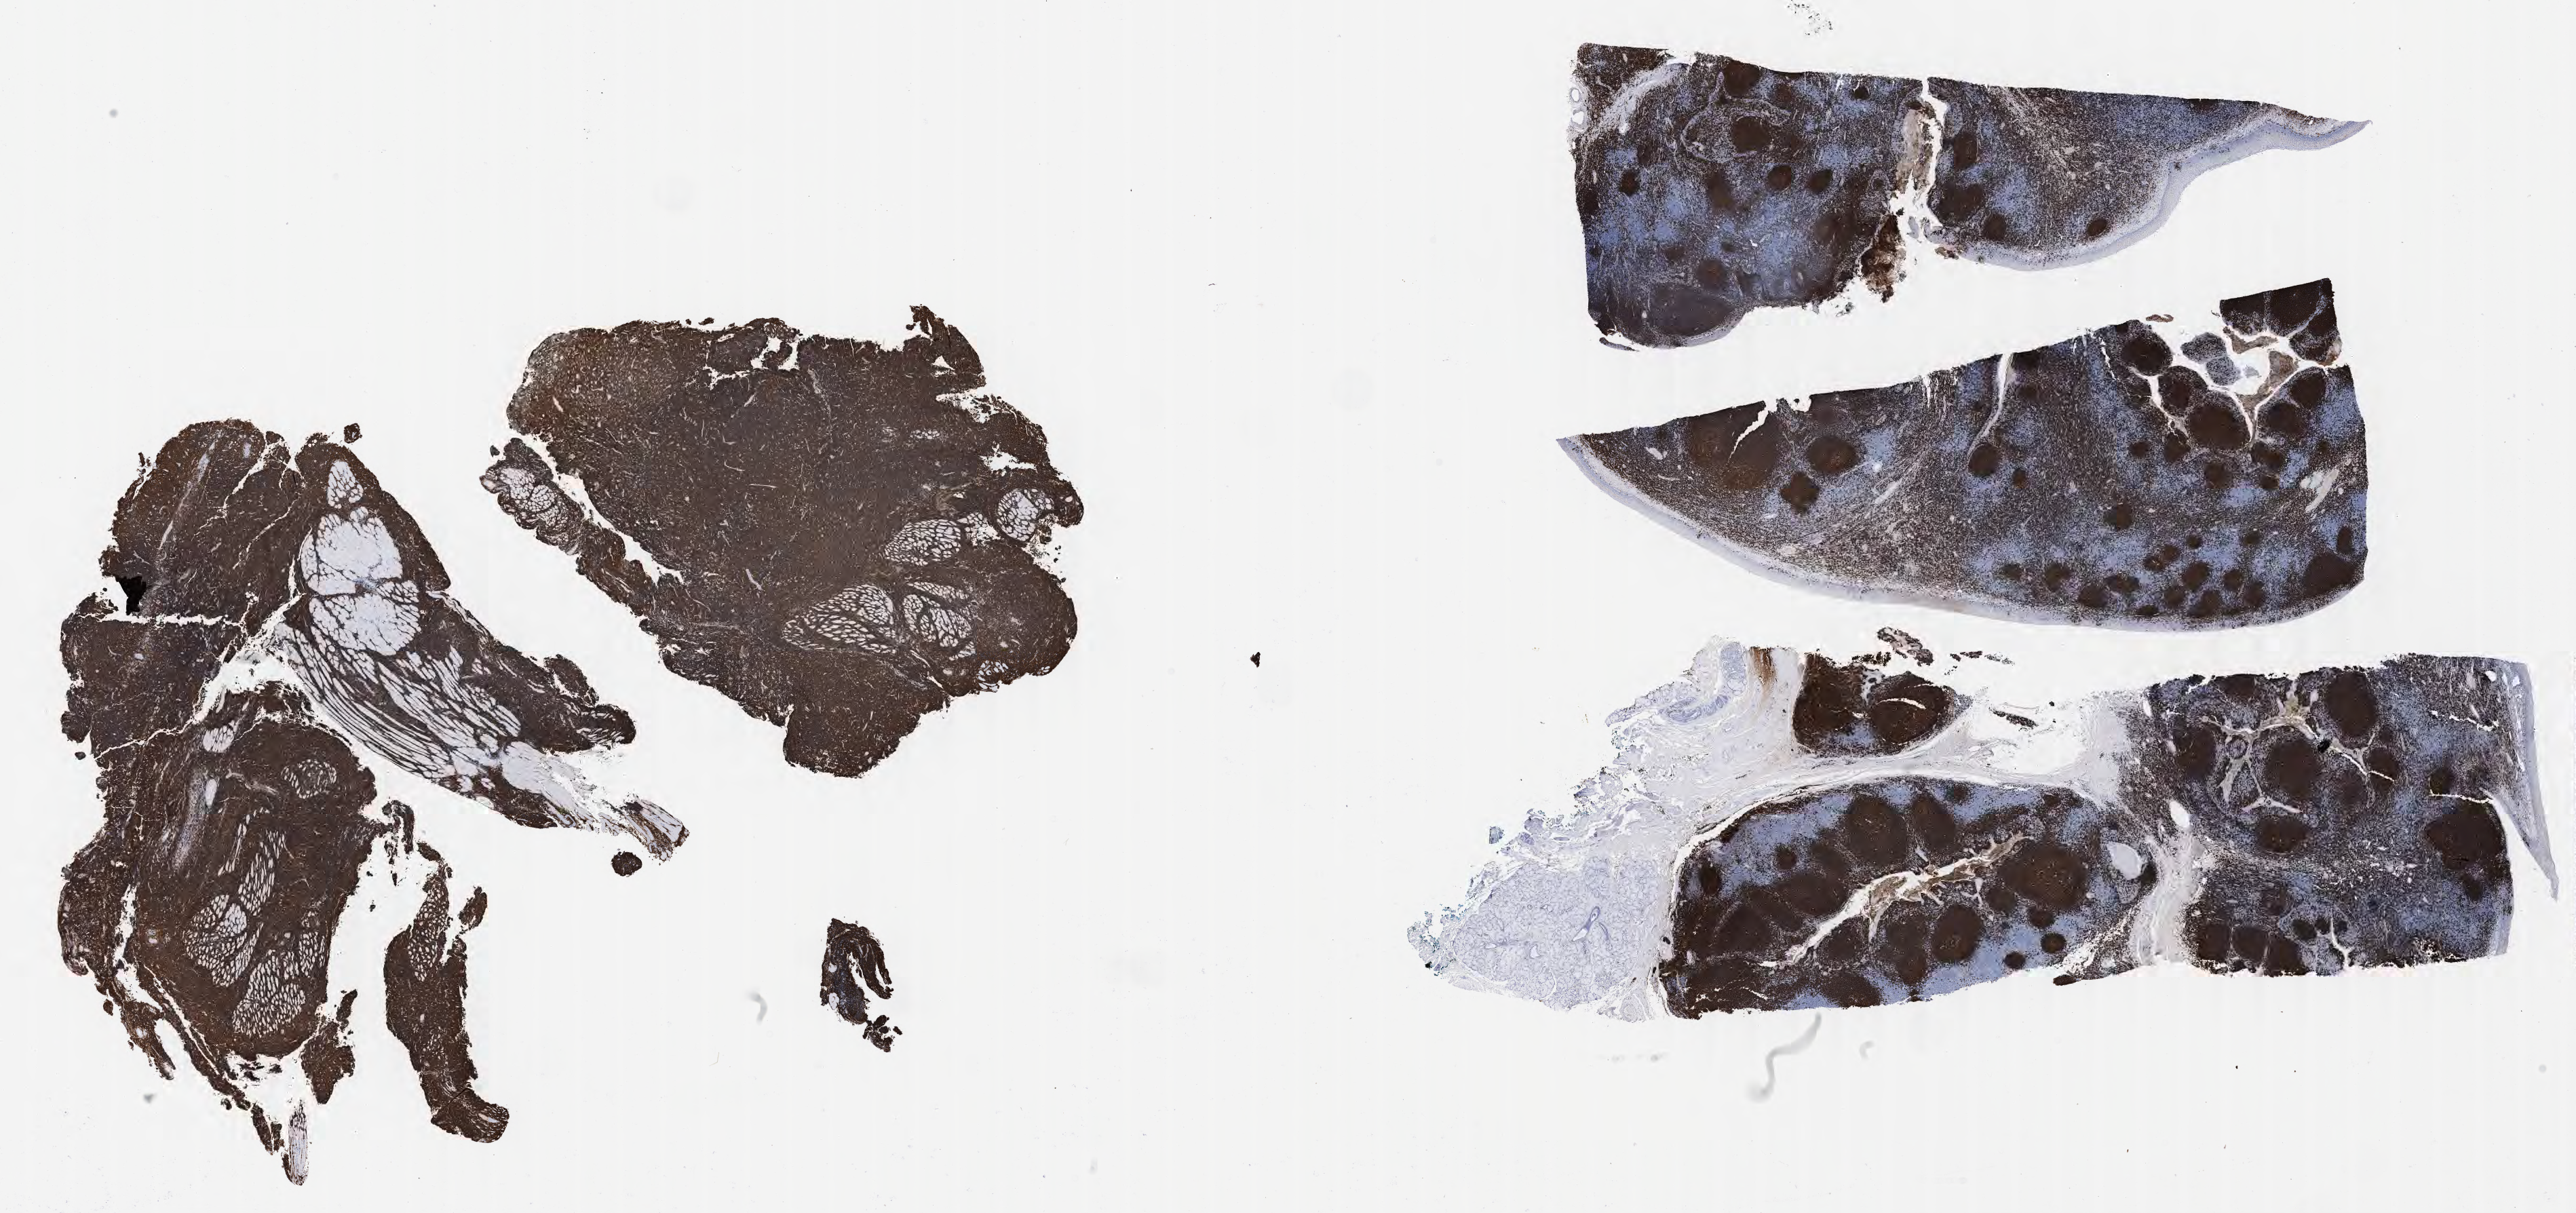
Whole-slide image, immunohistochemical stain for CD20 — a low-resolution overview of the entire scanned area, about 30.7 x 14.4 mm, specimen: tumor tissue, site: pelvis. Male, age 7 years at initial diagnosis.
Histologic diagnosis: Diffuse large B-cell lymphoma, NOS.